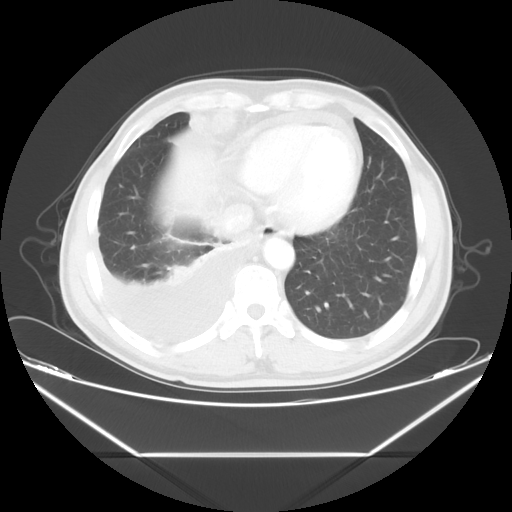
Chest CT, one axial slice; position 14 of 56 along the scan axis; reconstruction kernel STANDARD; lung window (W 1500 / L -600 HU); 5 mm slice thickness; 512 × 512 image matrix. Patient: male, 57 years. From the clinical record (not read from this slice): clinical TNM (as recorded): T2 N3 M1.
Structures marked on this image (bounding box drawn by a radiologist):
- lung tumour (recorded histology: adenocarcinoma): bounding box <191,107,243,139> (left, top, right, bottom; pixels)